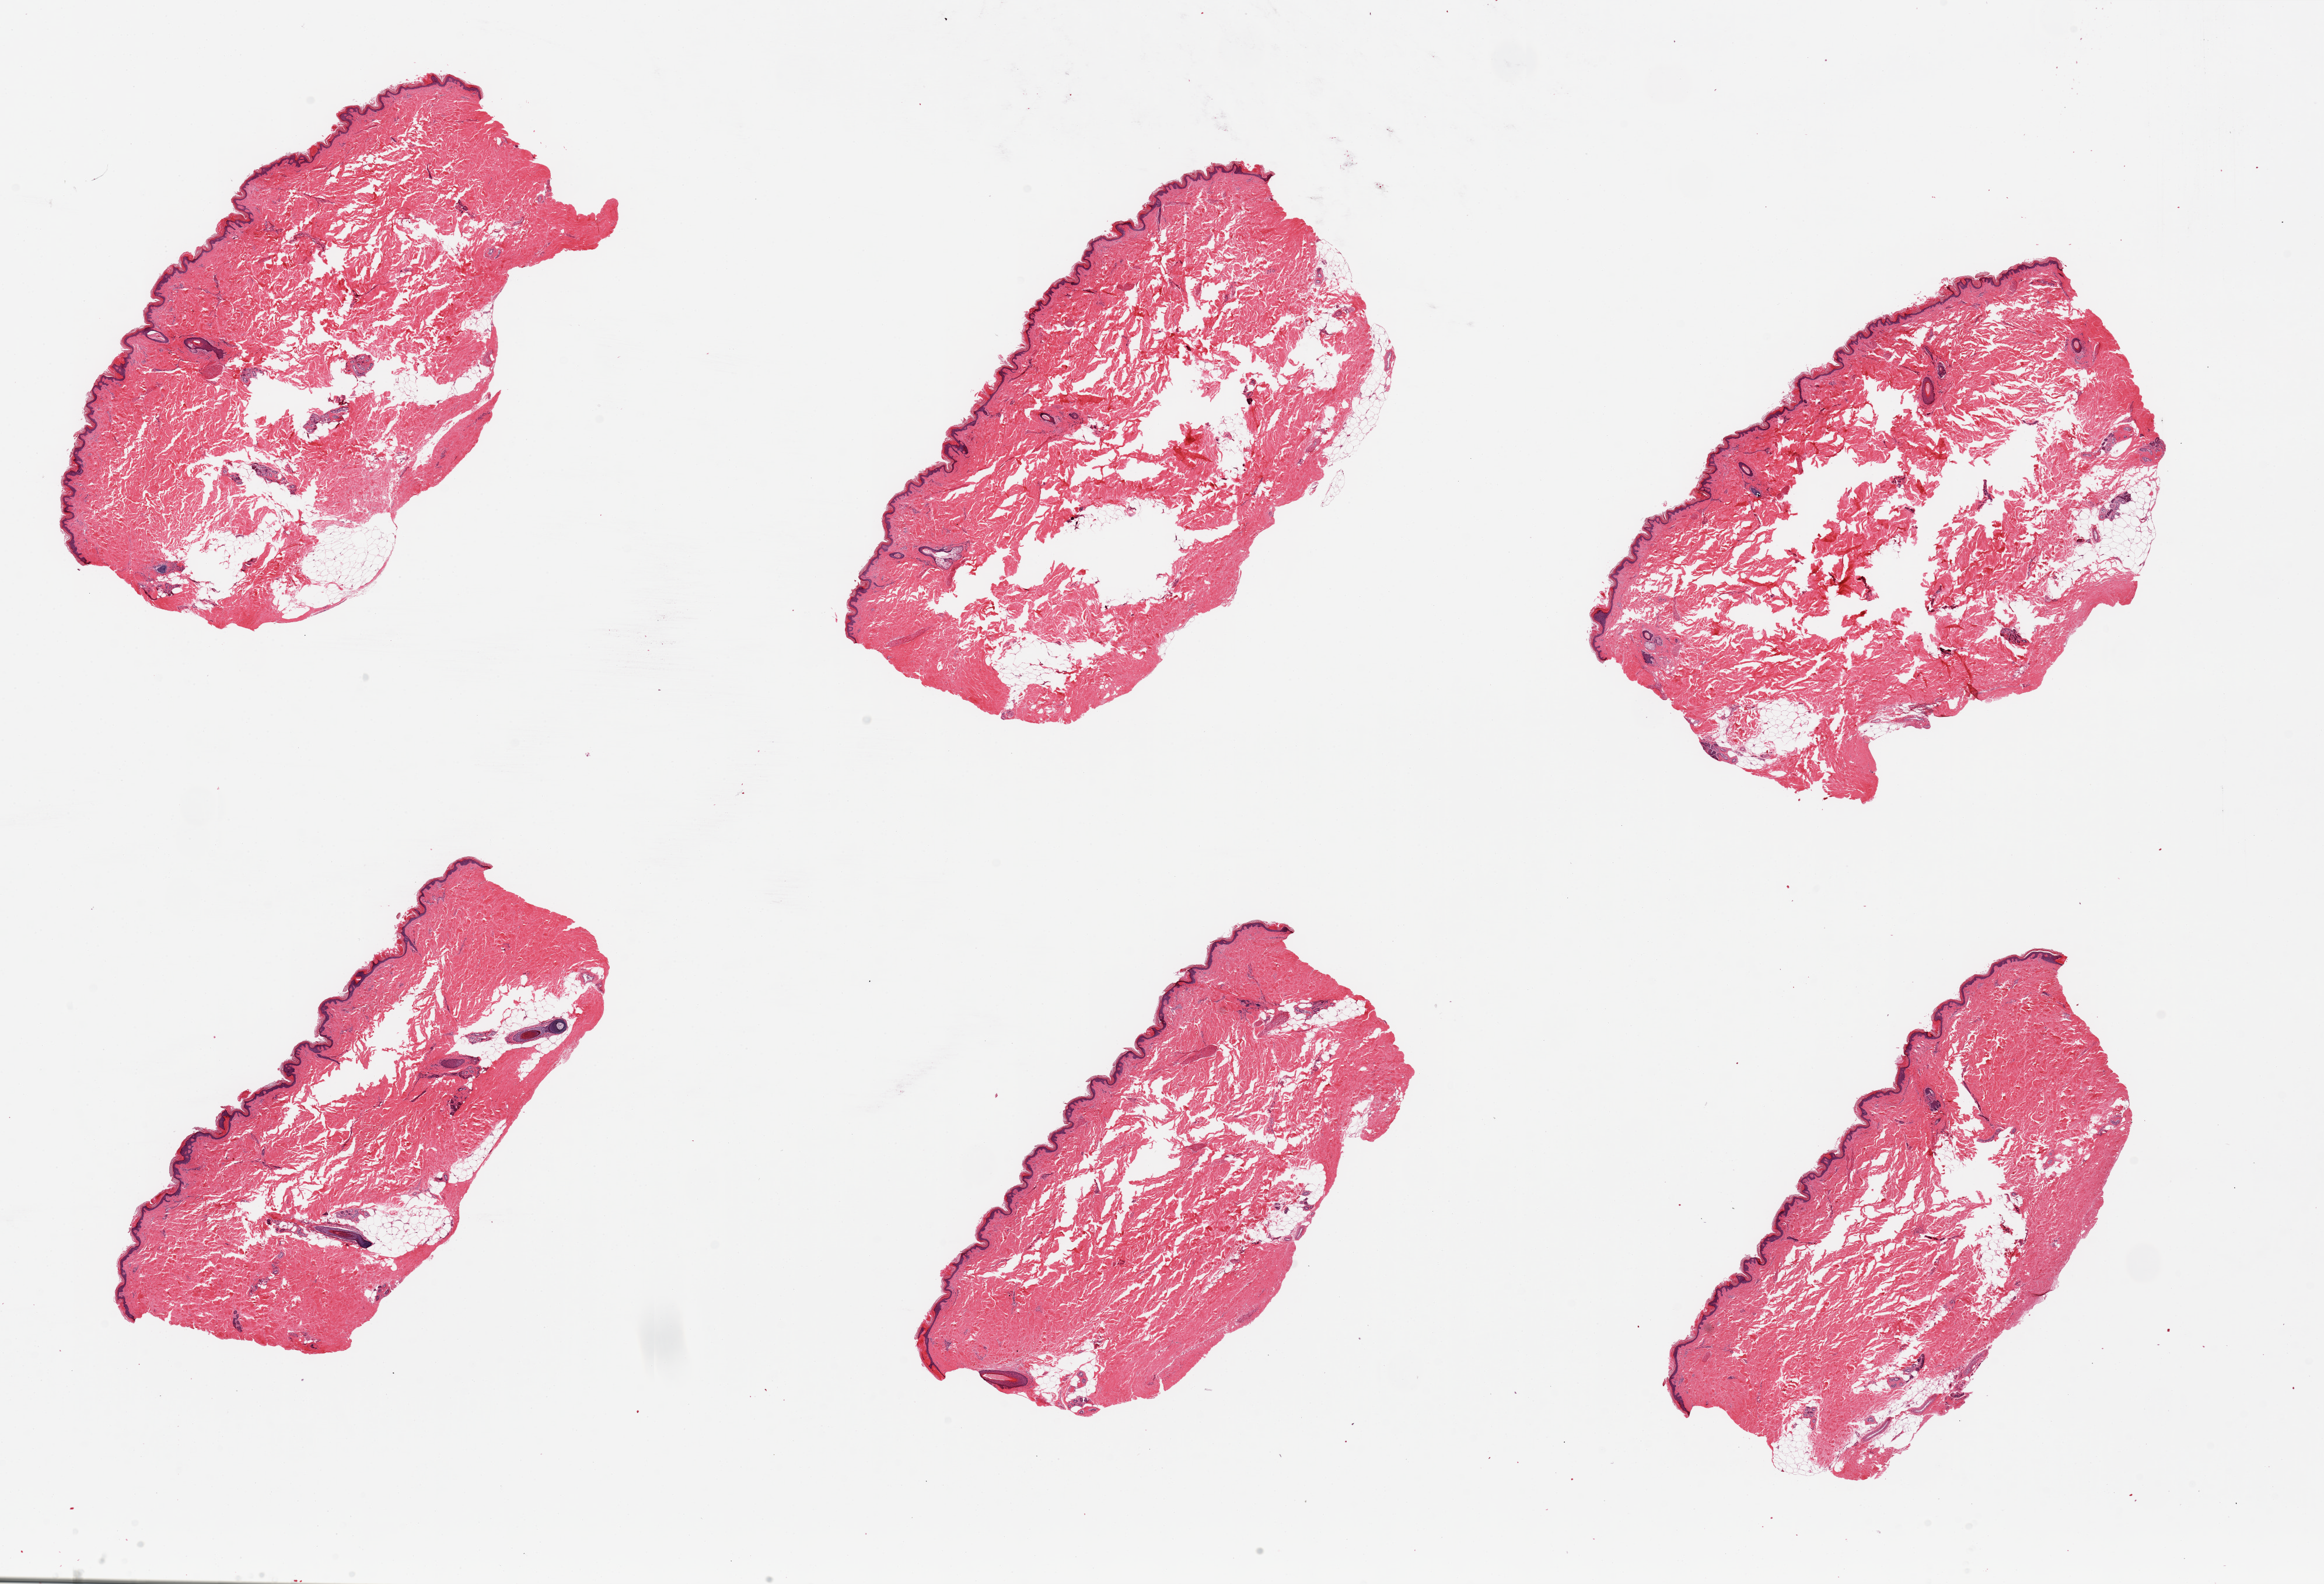
Digitized H&E-stained section — low-resolution overview of the scanned area, about 31.5 x 21.5 mm (from a 20x scan); PAXgene-fixed paraffin-embedded (PFPE) section; sampled site (target tissue): skin of lower leg; donor tissue sample. Donor sex: male.
- reviewer comment on this tissue sample: 6 pieces, squamous epithelium is ~50-75 microns; minimal adherent fat